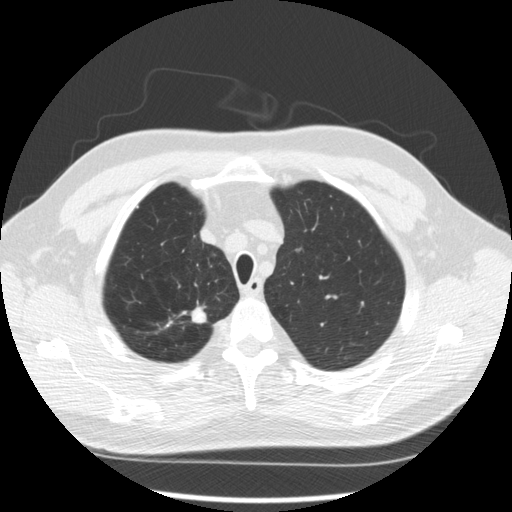
Low-dose screening chest CT, axial slice, second annual screen, lung window (W 1500 / L -600 HU), 2.5 mm slice thickness, slice 46 of 289 in the series. Male participant, aged 64 years at enrolment. Former smoker at enrolment.
Expert-annotated lung lesion, box from (x=171, y=299) to (x=217, y=334) px. The screening reader recorded 3 non-calcified nodules or masses ≥4 mm on this exam; which of them this box marks is not recorded. Official screen result: positive, other. Later outcome: lung cancer diagnosed 411 days after this screen (after the third annual screen) — adenocarcinoma, NOS, right upper lobe, moderately differentiated (G2), stage IA (AJCC 6th edition), 14 mm at pathology.